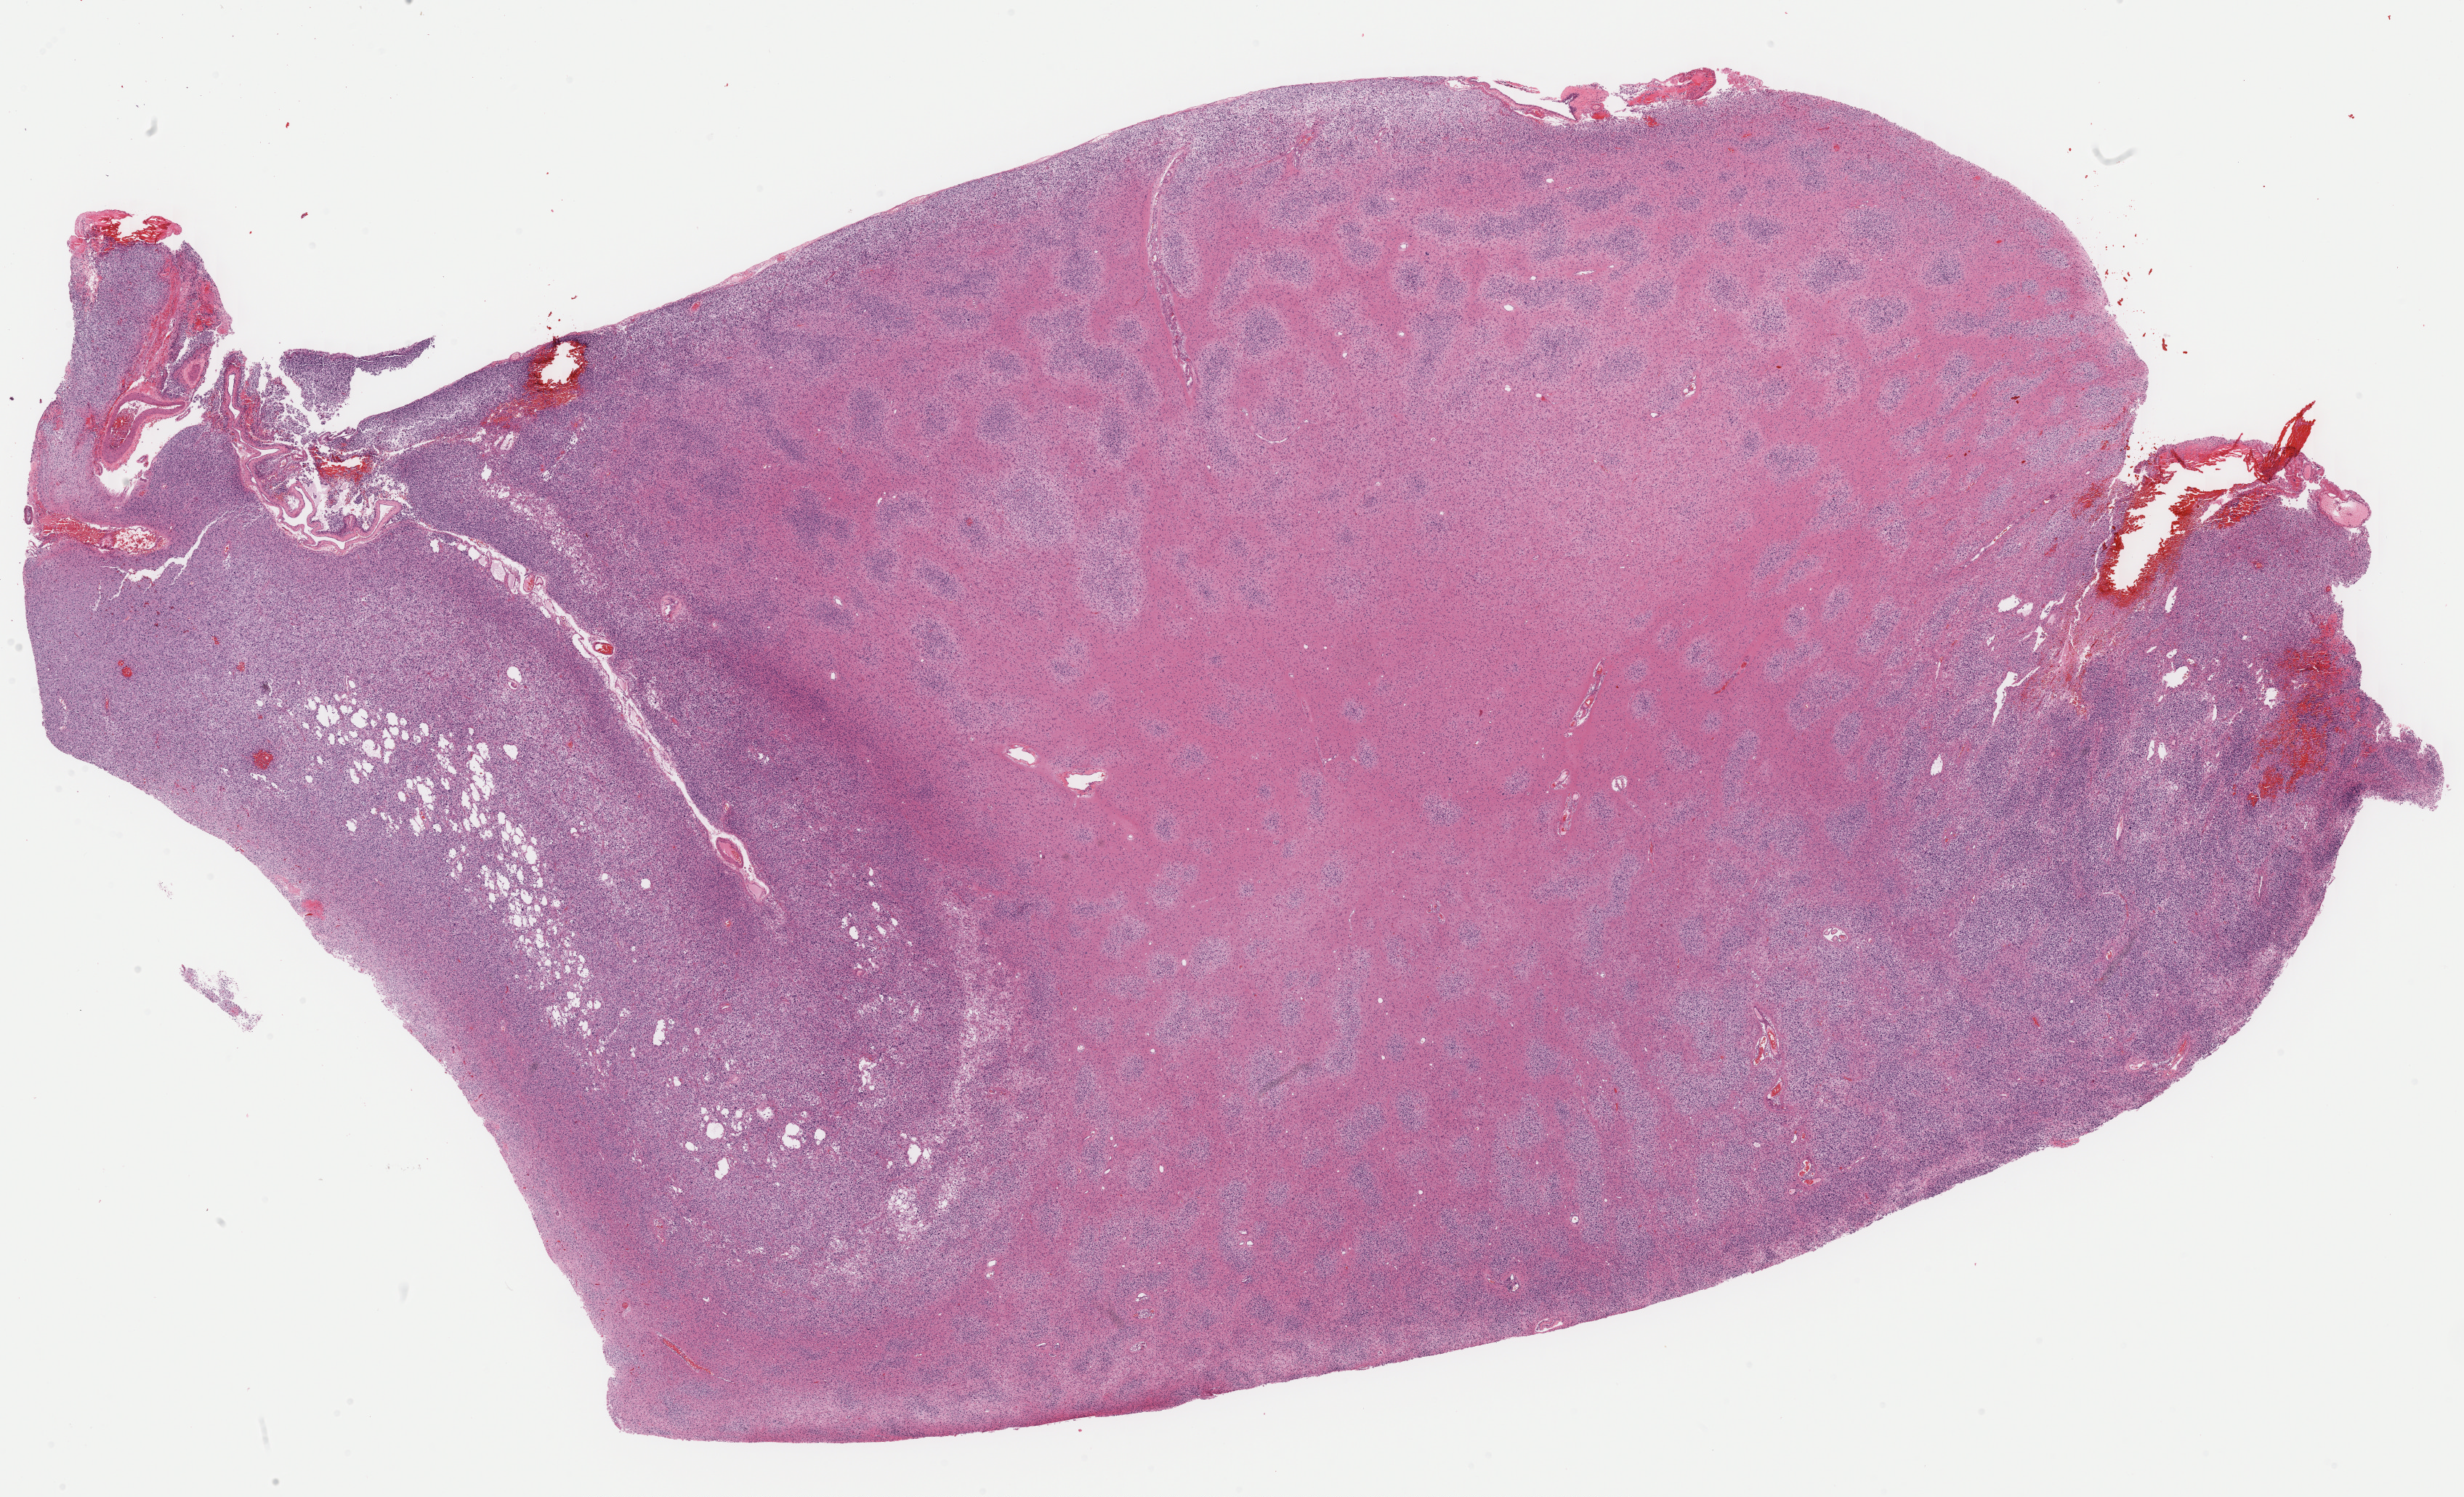
Whole-slide histology image, H&E — low-resolution overview of the scanned area, about 26.7 x 16.2 mm (from a 40x scan); formalin-fixed paraffin-embedded (FFPE) diagnostic section; primary tumour sample from the brain. Male patient; age at initial diagnosis 36 years. Histologic grade: G3 (poorly differentiated).
Pathologic diagnosis: Mixed glioma (cerebrum). Laterality: right.